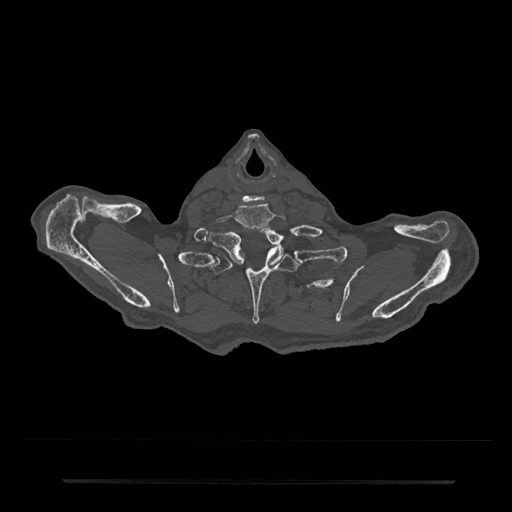
CT including the spine, one axial slice; slice 711 of 797 in the series (ordered by position); bone window (W 1800 / L 400 HU); 512 × 512 image matrix. Male patient, age 74 years. From the clinical record (not read from this slice): primary cancer: prostate.
Annotated regions visible in this slice (semi-automatic segmentation, software-assisted and operator-edited):
- T1 vertebra: box from (x=209, y=225) to (x=284, y=268) px
- T2 vertebra: (x=210, y=248)–(x=304, y=325)